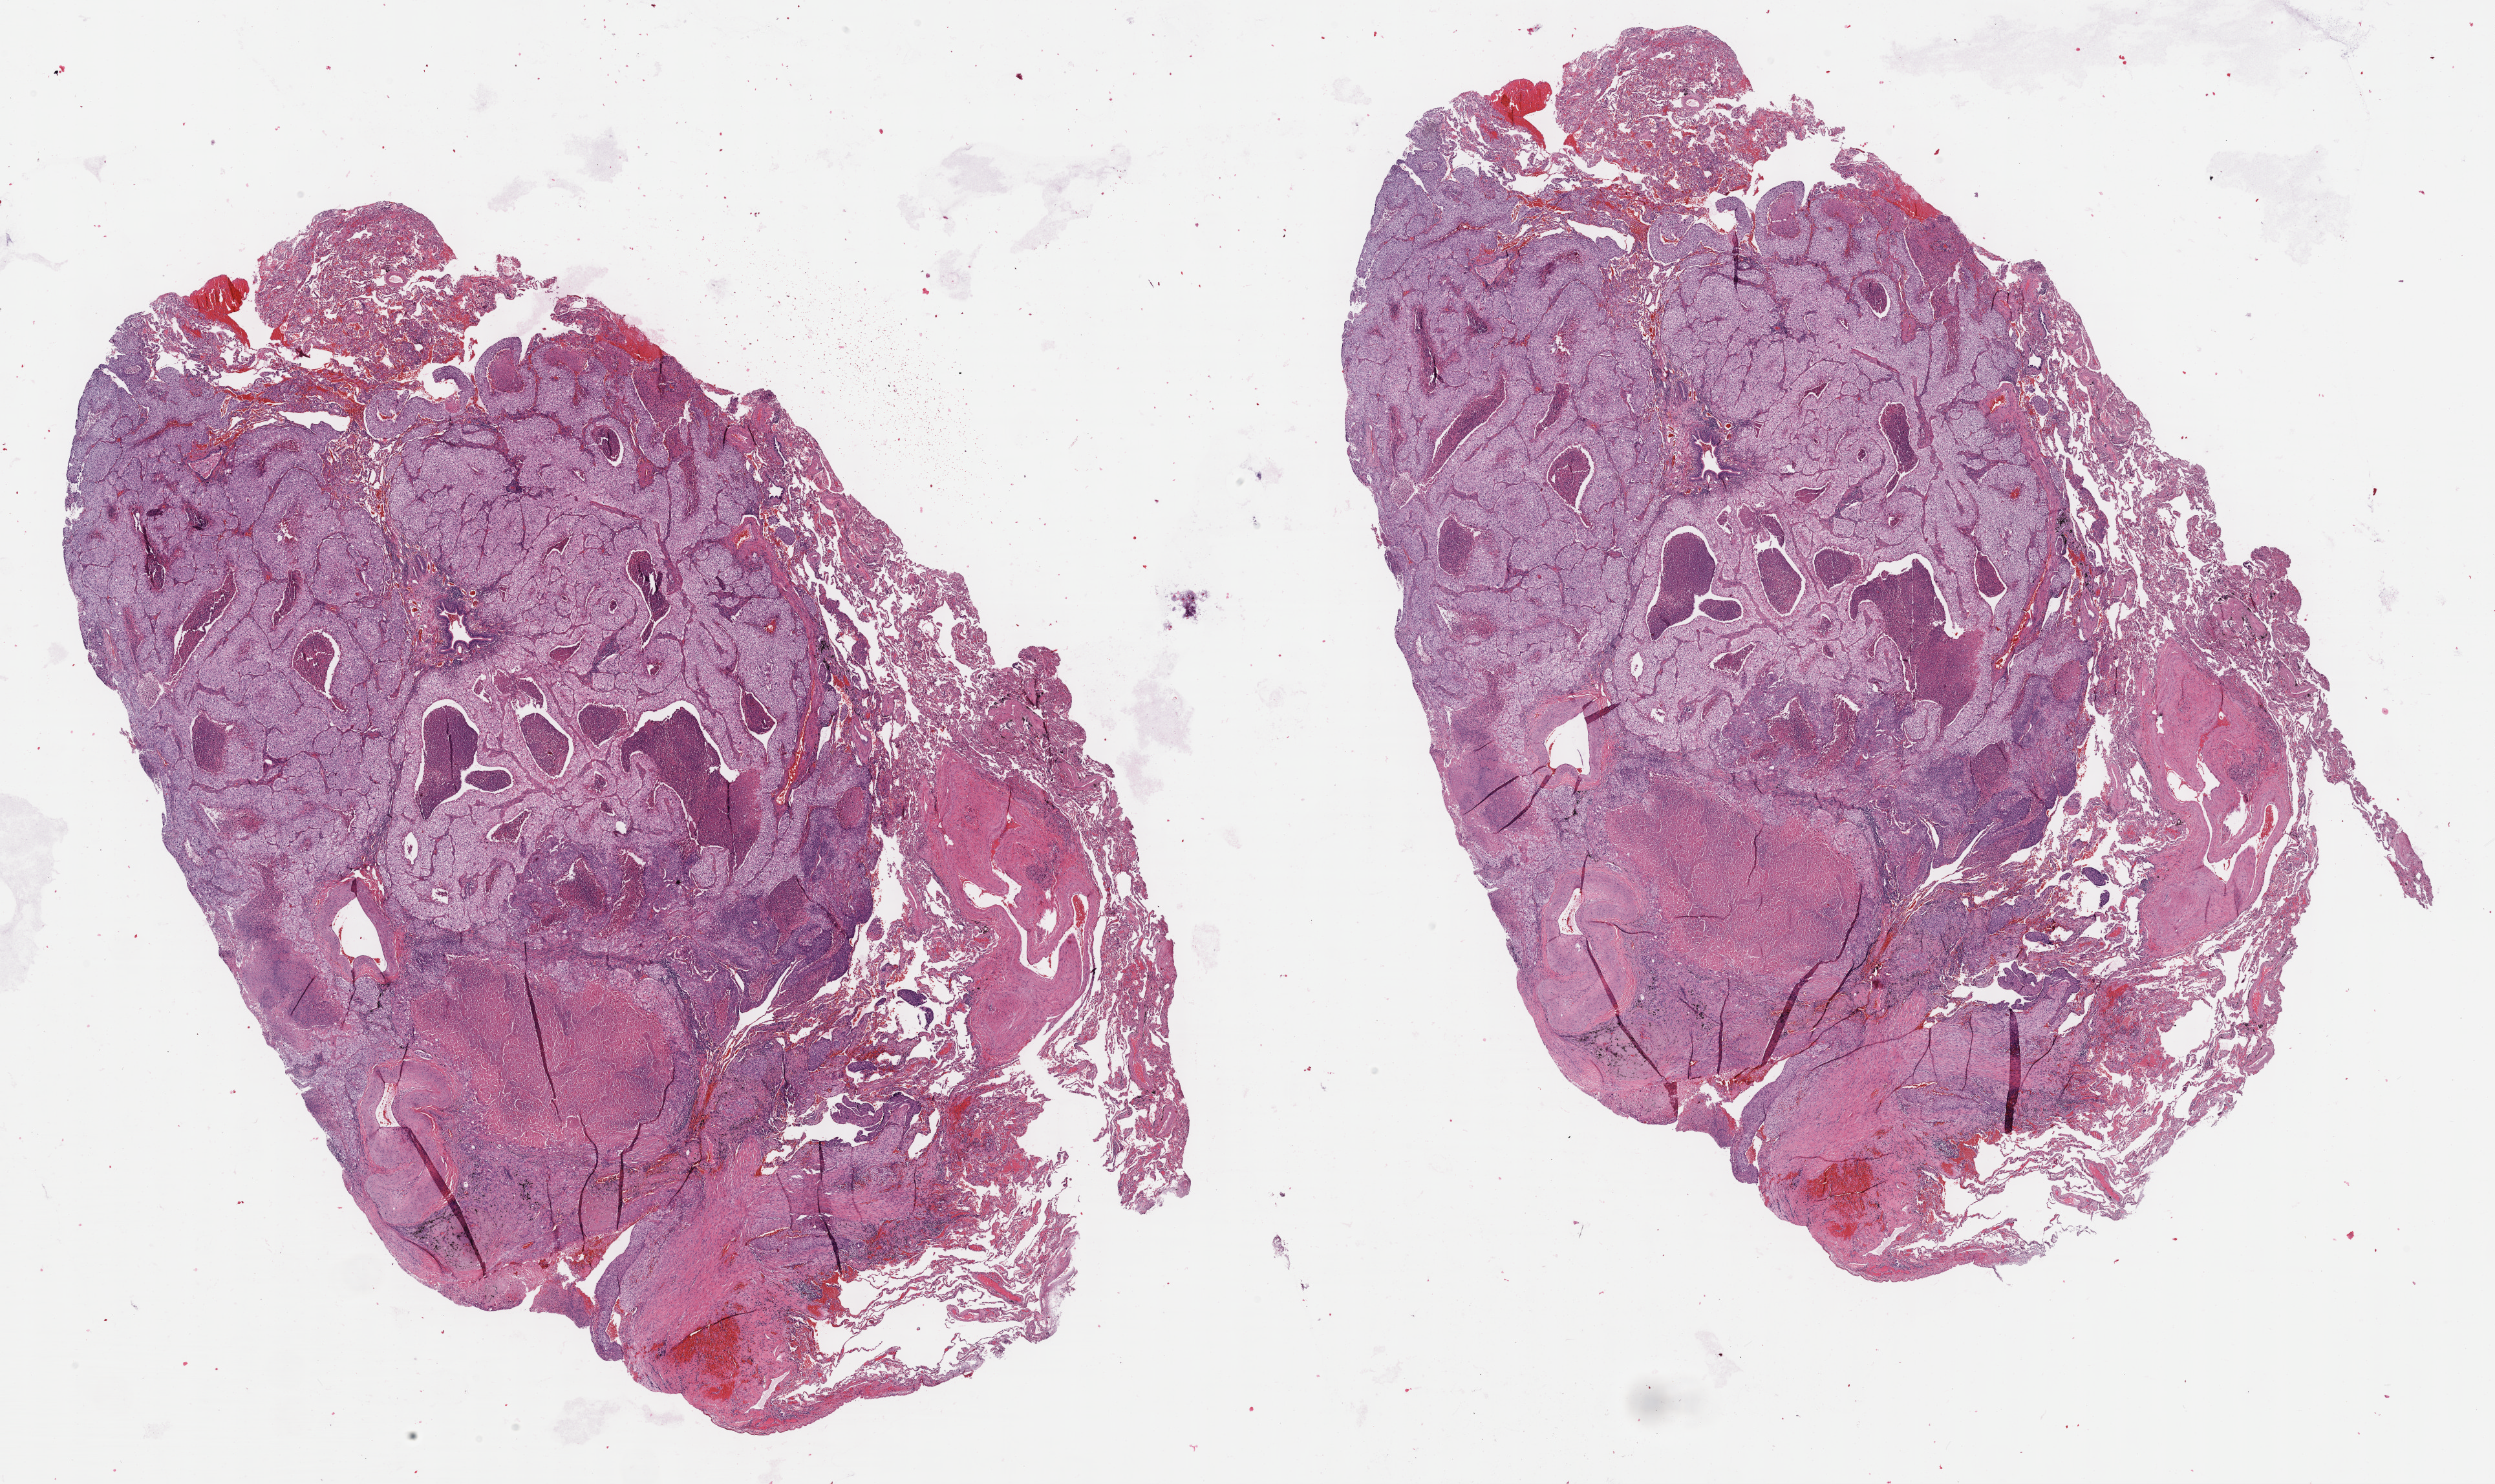
Whole-slide histology image, H&E-stained — a low-resolution overview of the entire scanned area, about 31.2 x 18.6 mm; FFPE section; primary tumour sample from the lung. Male, age 70 years at initial diagnosis.
Histologic diagnosis: Squamous cell carcinoma, NOS (lower lobe, lung). AJCC pathologic stage: IA (6th edition).